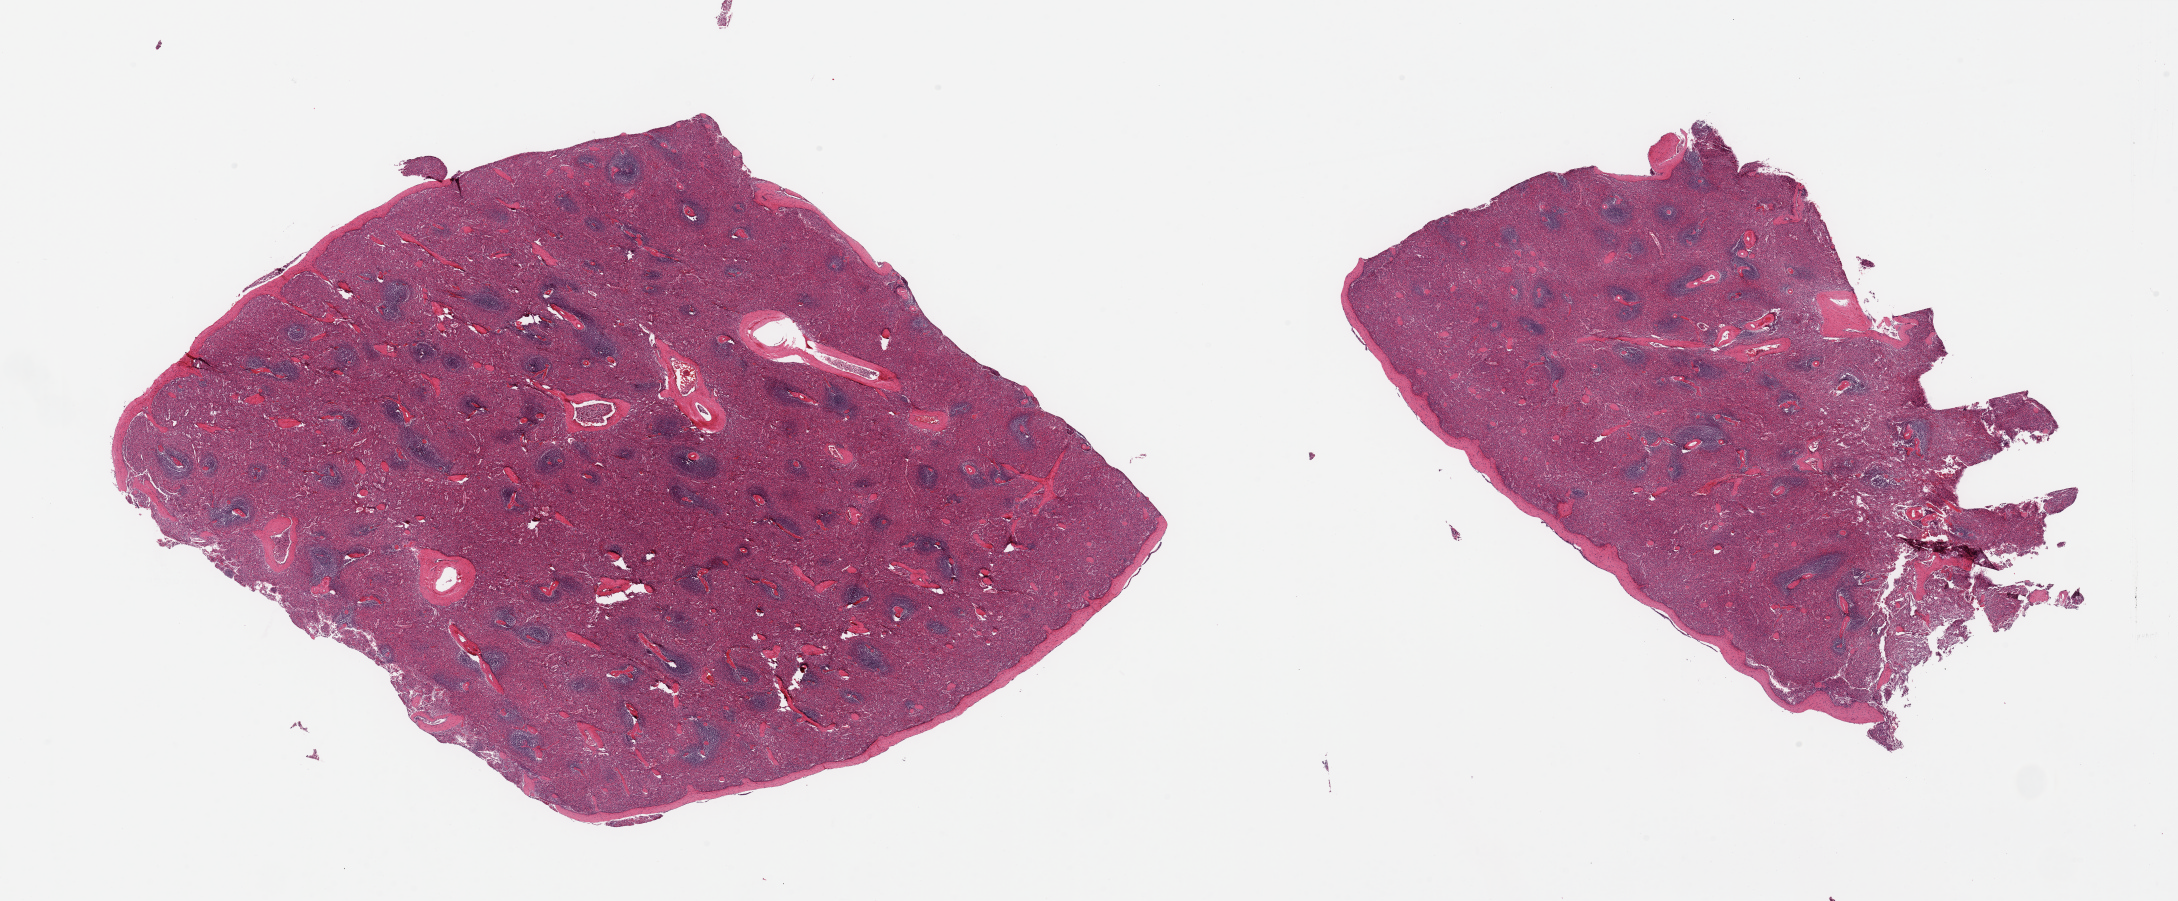
Digitized hematoxylin and eosin (H&E)-stained section, shown as a low-resolution overview of the whole scanned area (about 34.5 x 14.3 mm, slide scanned at 20x); PAXgene-fixed paraffin-embedded (PFPE) section; sampled site (target tissue): spleen; donor tissue sample. Donor: female.
Reviewer comment on this tissue sample: 2 pieces; mild congestion.